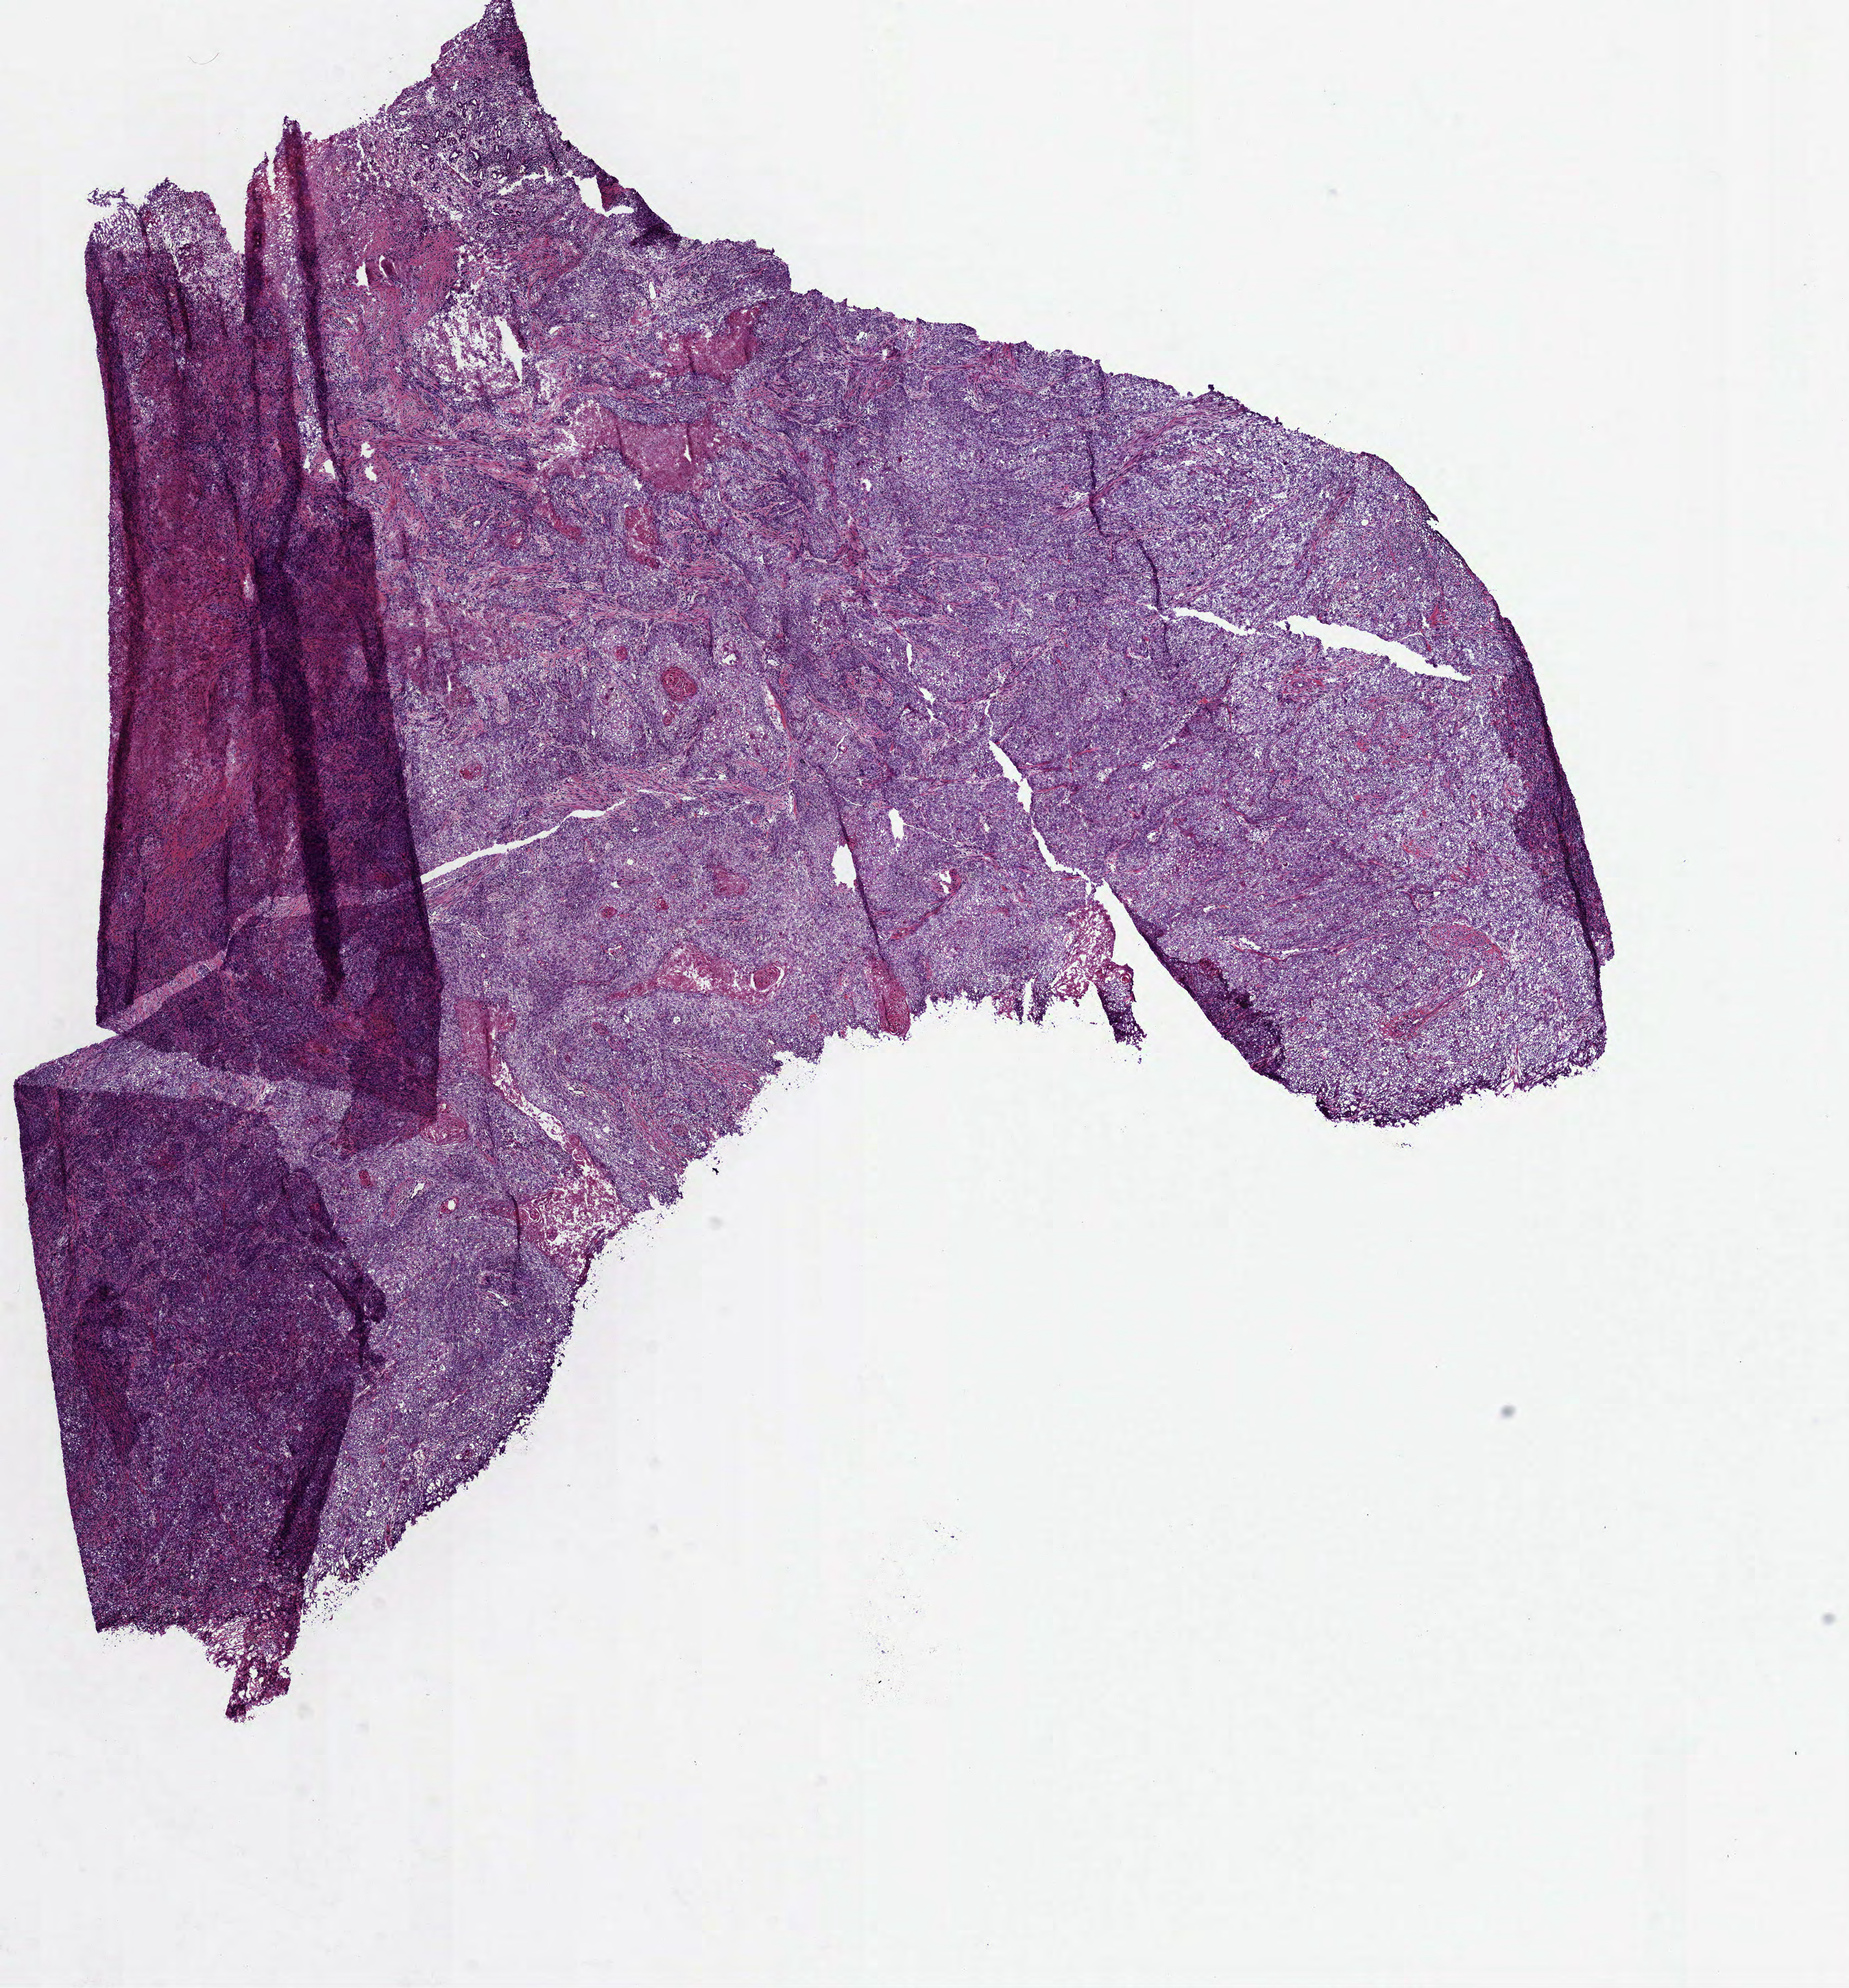
Whole-slide histology image, Hematoxylin and eosin (H&E) stained, a low-resolution overview of the entire scanned area, about 10.9 x 11.7 mm (slide scanned at 40x); frozen section from the bottom of the tissue portion; head and neck, primary tumour sample. Patient: male, age at initial diagnosis 58 years.
Diagnosis: Squamous cell carcinoma, NOS (larynx, NOS).